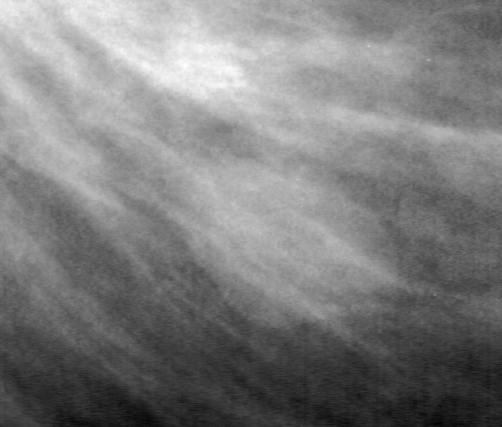
Region of interest cut from a scanned film mammogram (one marked finding); right breast; MLO view; BI-RADS breast density category 4 (scale 1–4).
Mass, shape oval, margins circumscribed; BI-RADS assessment category 4; pathology result (as recorded, not read from the image): benign.